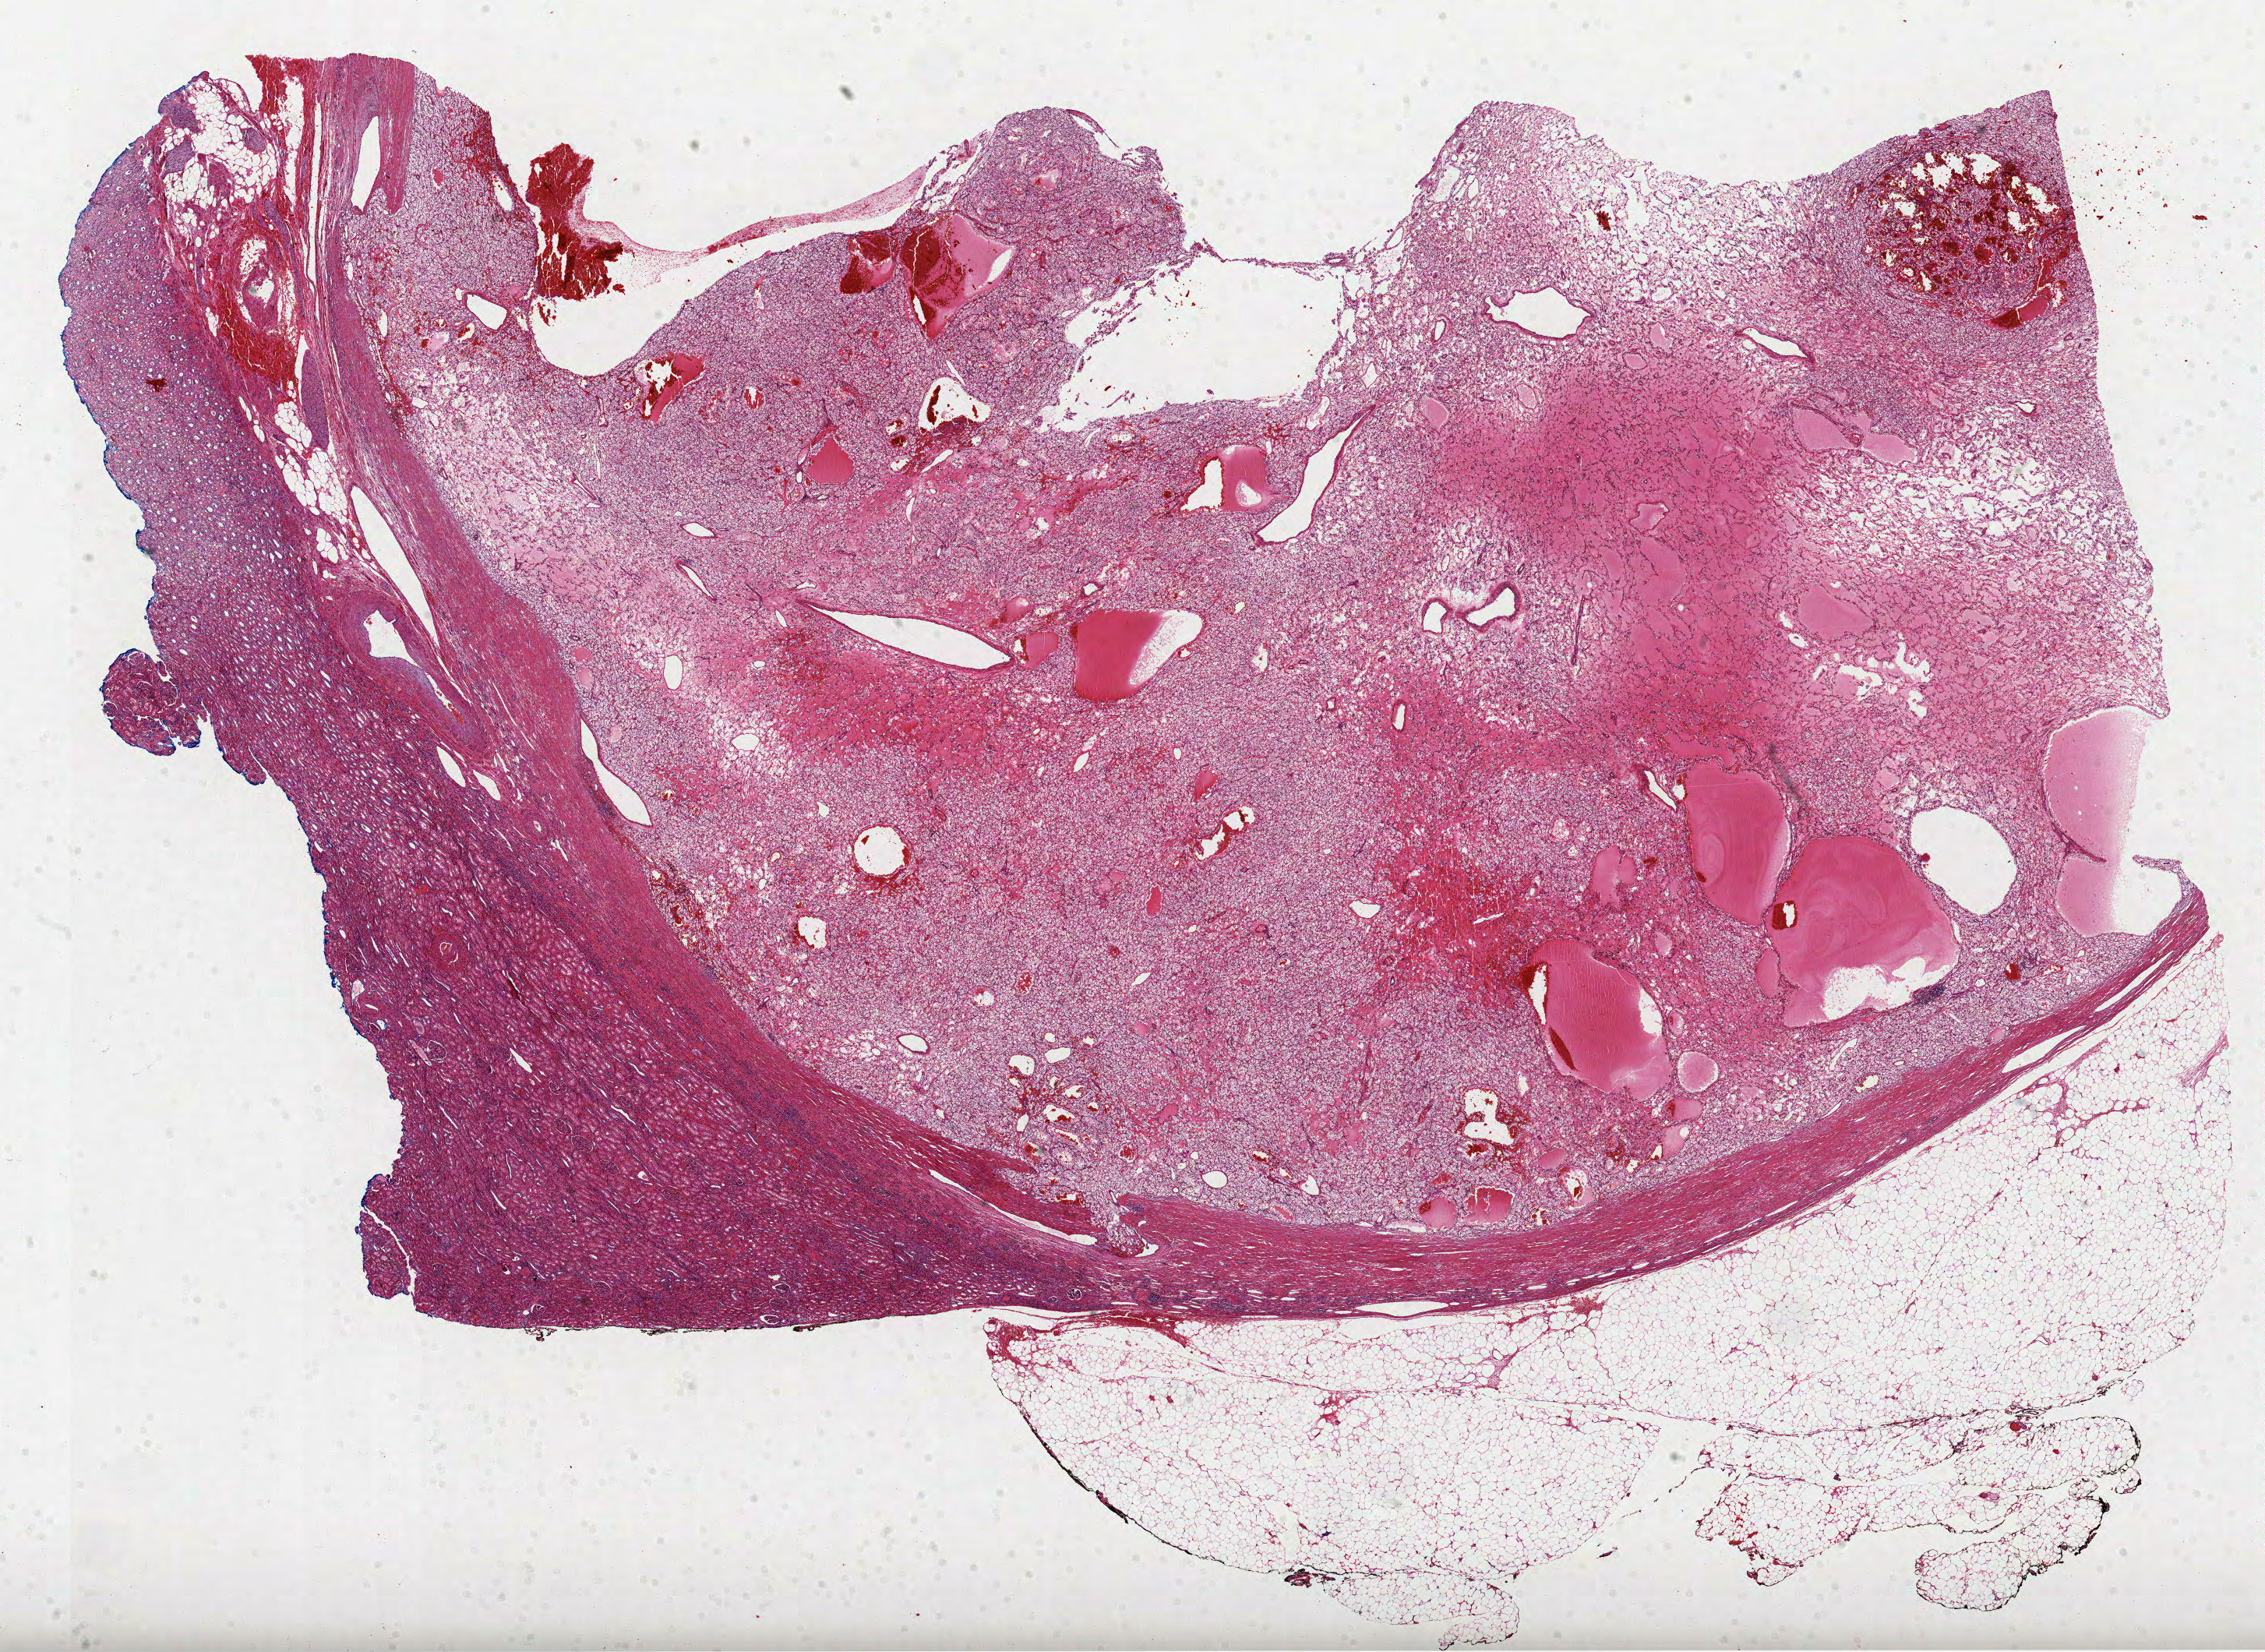
Whole-slide histology image, H&E-stained, shown as a low-resolution overview of the whole scanned area (about 23.4 x 17.1 mm, slide scanned at 40x), formalin-fixed paraffin-embedded (FFPE) diagnostic section, sample: primary tumour, kidney. Male, age 63 years at initial diagnosis. Histologic grade: G4 (undifferentiated).
Laterality: left. AJCC pathologic stage: III. Diagnosis: Clear cell adenocarcinoma, NOS.